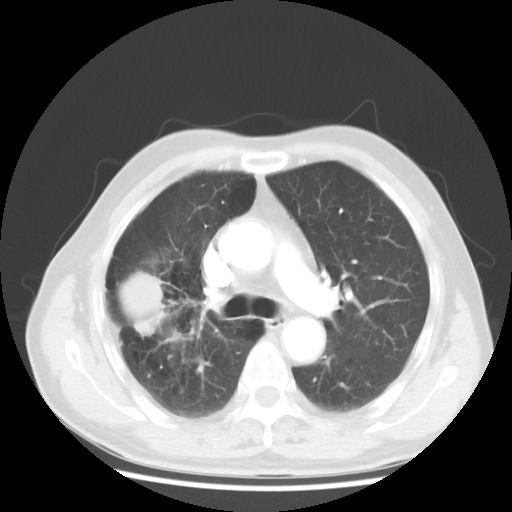
Chest CT, one axial slice. Position 31 of 50 along the scan axis. Lung window (W 1500 / L -600 HU). 5 mm slice thickness. 512 × 512 image matrix, field of view 360 × 360 mm. Patient: male, 69 years. Case-level facts recorded for this patient, not image findings: clinical TNM (as recorded): T3 N0 M0; histopathological grade: G3.
Annotated regions visible in this slice (rectangle marked by the reading radiologist):
- lung tumour (recorded histology: adenocarcinoma): bounding box <110,268,175,341> (left, top, right, bottom; pixels)